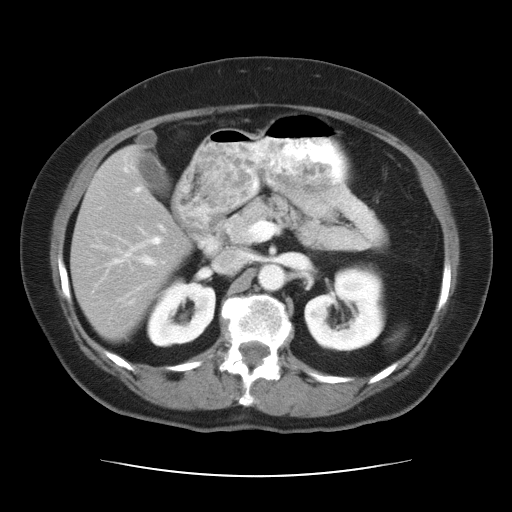
Contrast-enhanced abdominal CT, one axial slice; position 16 of 34 along the scan axis; reconstruction kernel STANDARD; intravenous contrast given; soft-tissue window (W 400 / L 40 HU); 512 × 512 image matrix. Female patient, age 65 years. From the clinical record (not read from this slice): diagnosis: colorectal cancer liver metastases, imaged before liver resection; multiple liver metastases: yes; largest metastasis: 2.2 cm; chemotherapy before resection: yes.
Outlined on this slice (manually delineated by an expert):
- hepatic veins: box from (x=133, y=186) to (x=259, y=272) px
- liver: (x=73, y=150)–(x=189, y=338)
- planned liver remnant (the part of the liver to remain after resection): (x=73, y=150)–(x=189, y=338)
- portal vein (with intrahepatic branches): (x=113, y=224)–(x=165, y=264)